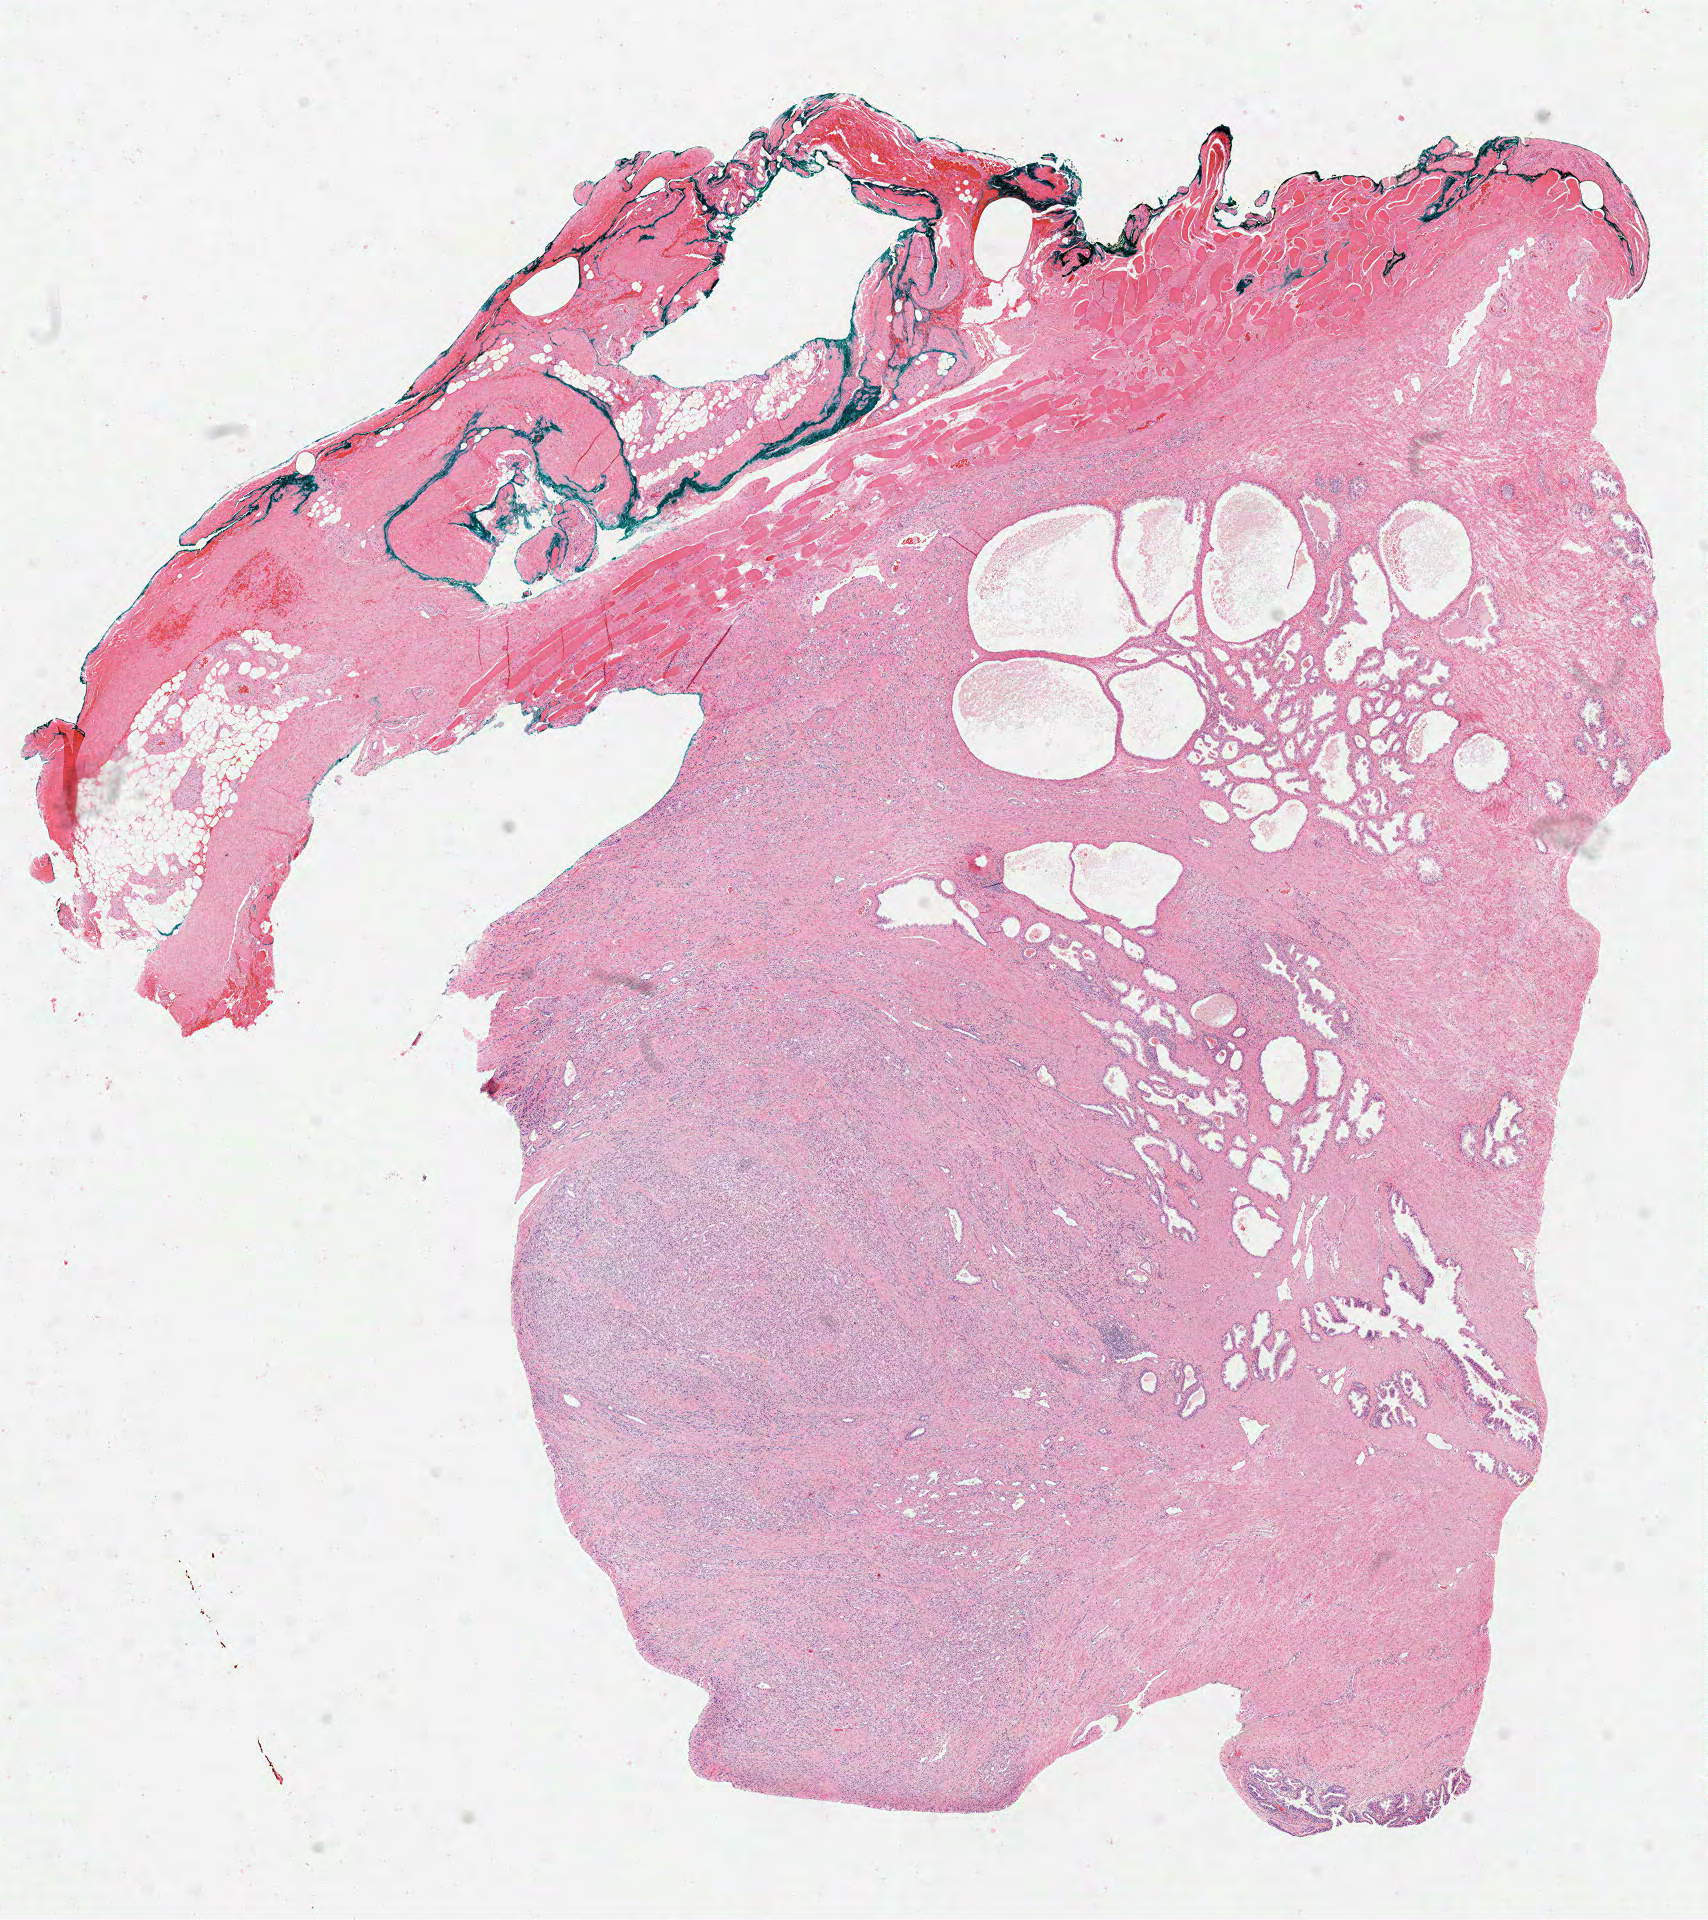
Whole-slide histology image, H&E — shown as a low-resolution overview of the whole scanned area (about 13.8 x 15.5 mm, slide scanned at 40x); formalin-fixed paraffin-embedded (FFPE) diagnostic section; primary tumour sample from the prostate. Patient: male, age at initial diagnosis 44 years. Gleason score: 10 (5+5).
• histologic diagnosis: Acinar cell carcinoma (prostate gland)
• lymph nodes positive (case pathology): 0 of 10 examined
• laterality: bilateral